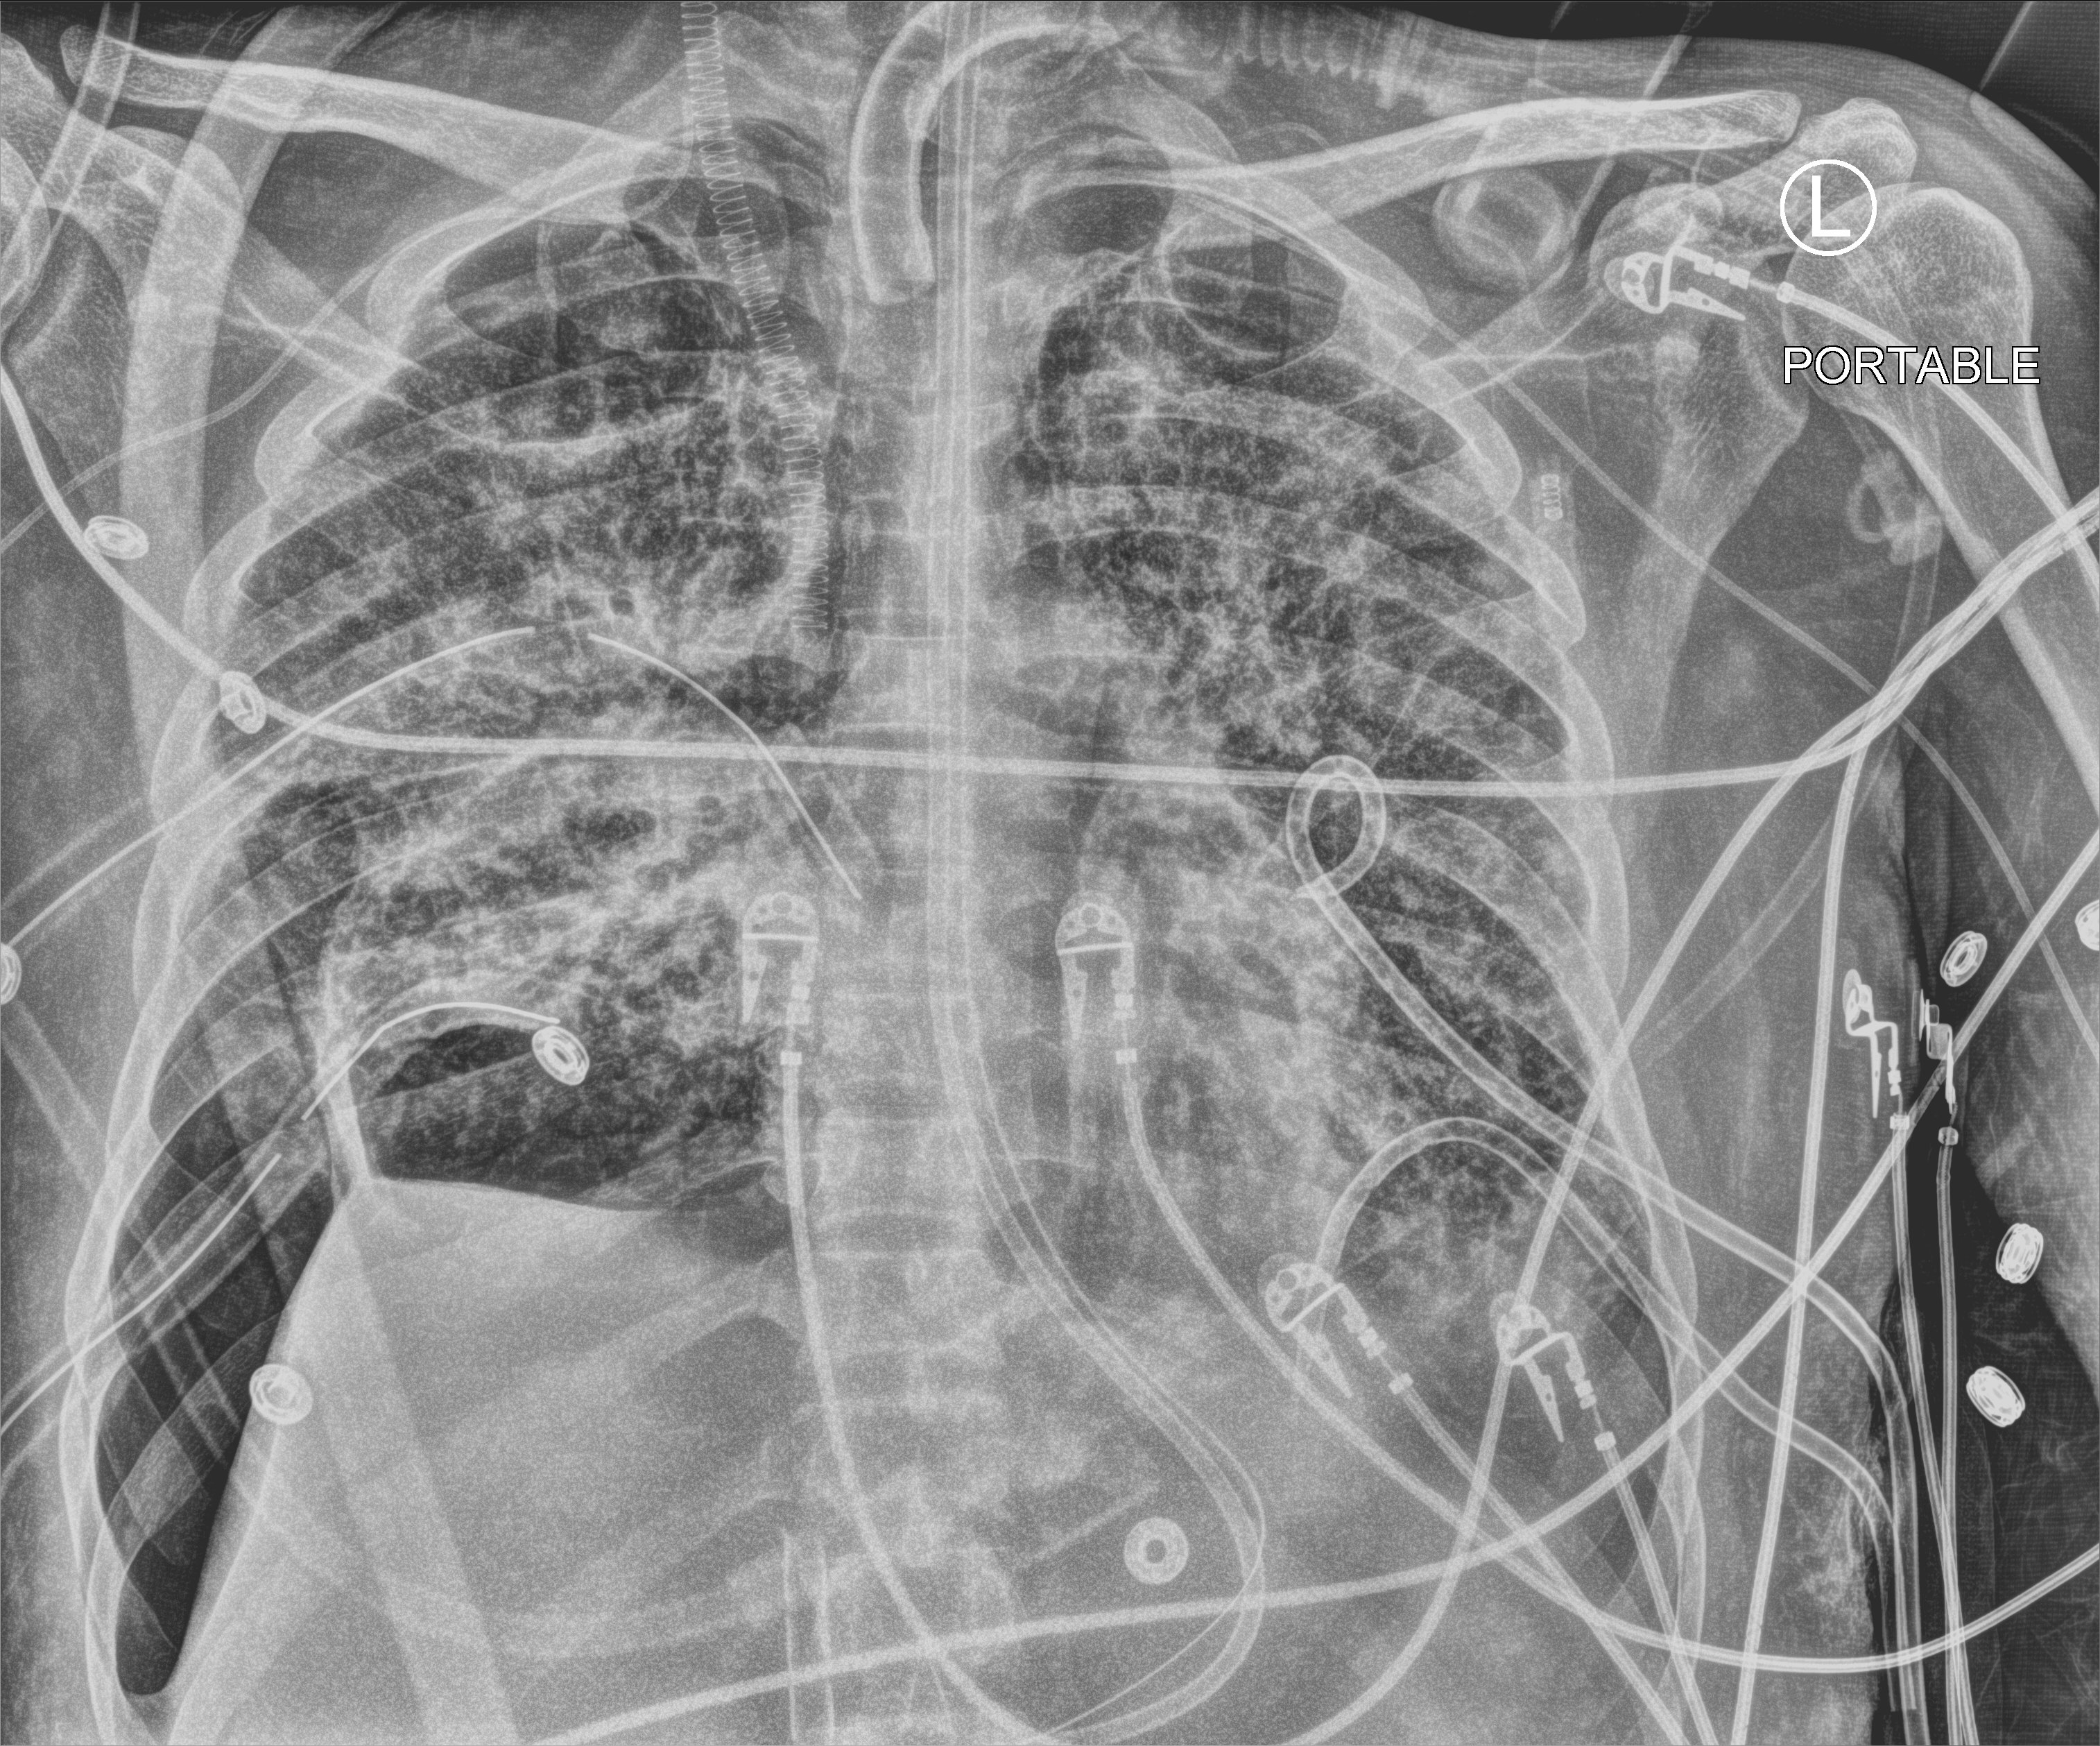
Portable chest radiograph; anteroposterior (AP) projection. Adult patient hospitalised with COVID-19, age 18–59 years.
From the hospital-stay record, not from the radiograph (when in the stay this image was taken is not recorded): mechanically ventilated during this hospital stay: yes; chronic kidney disease (admission record): no.